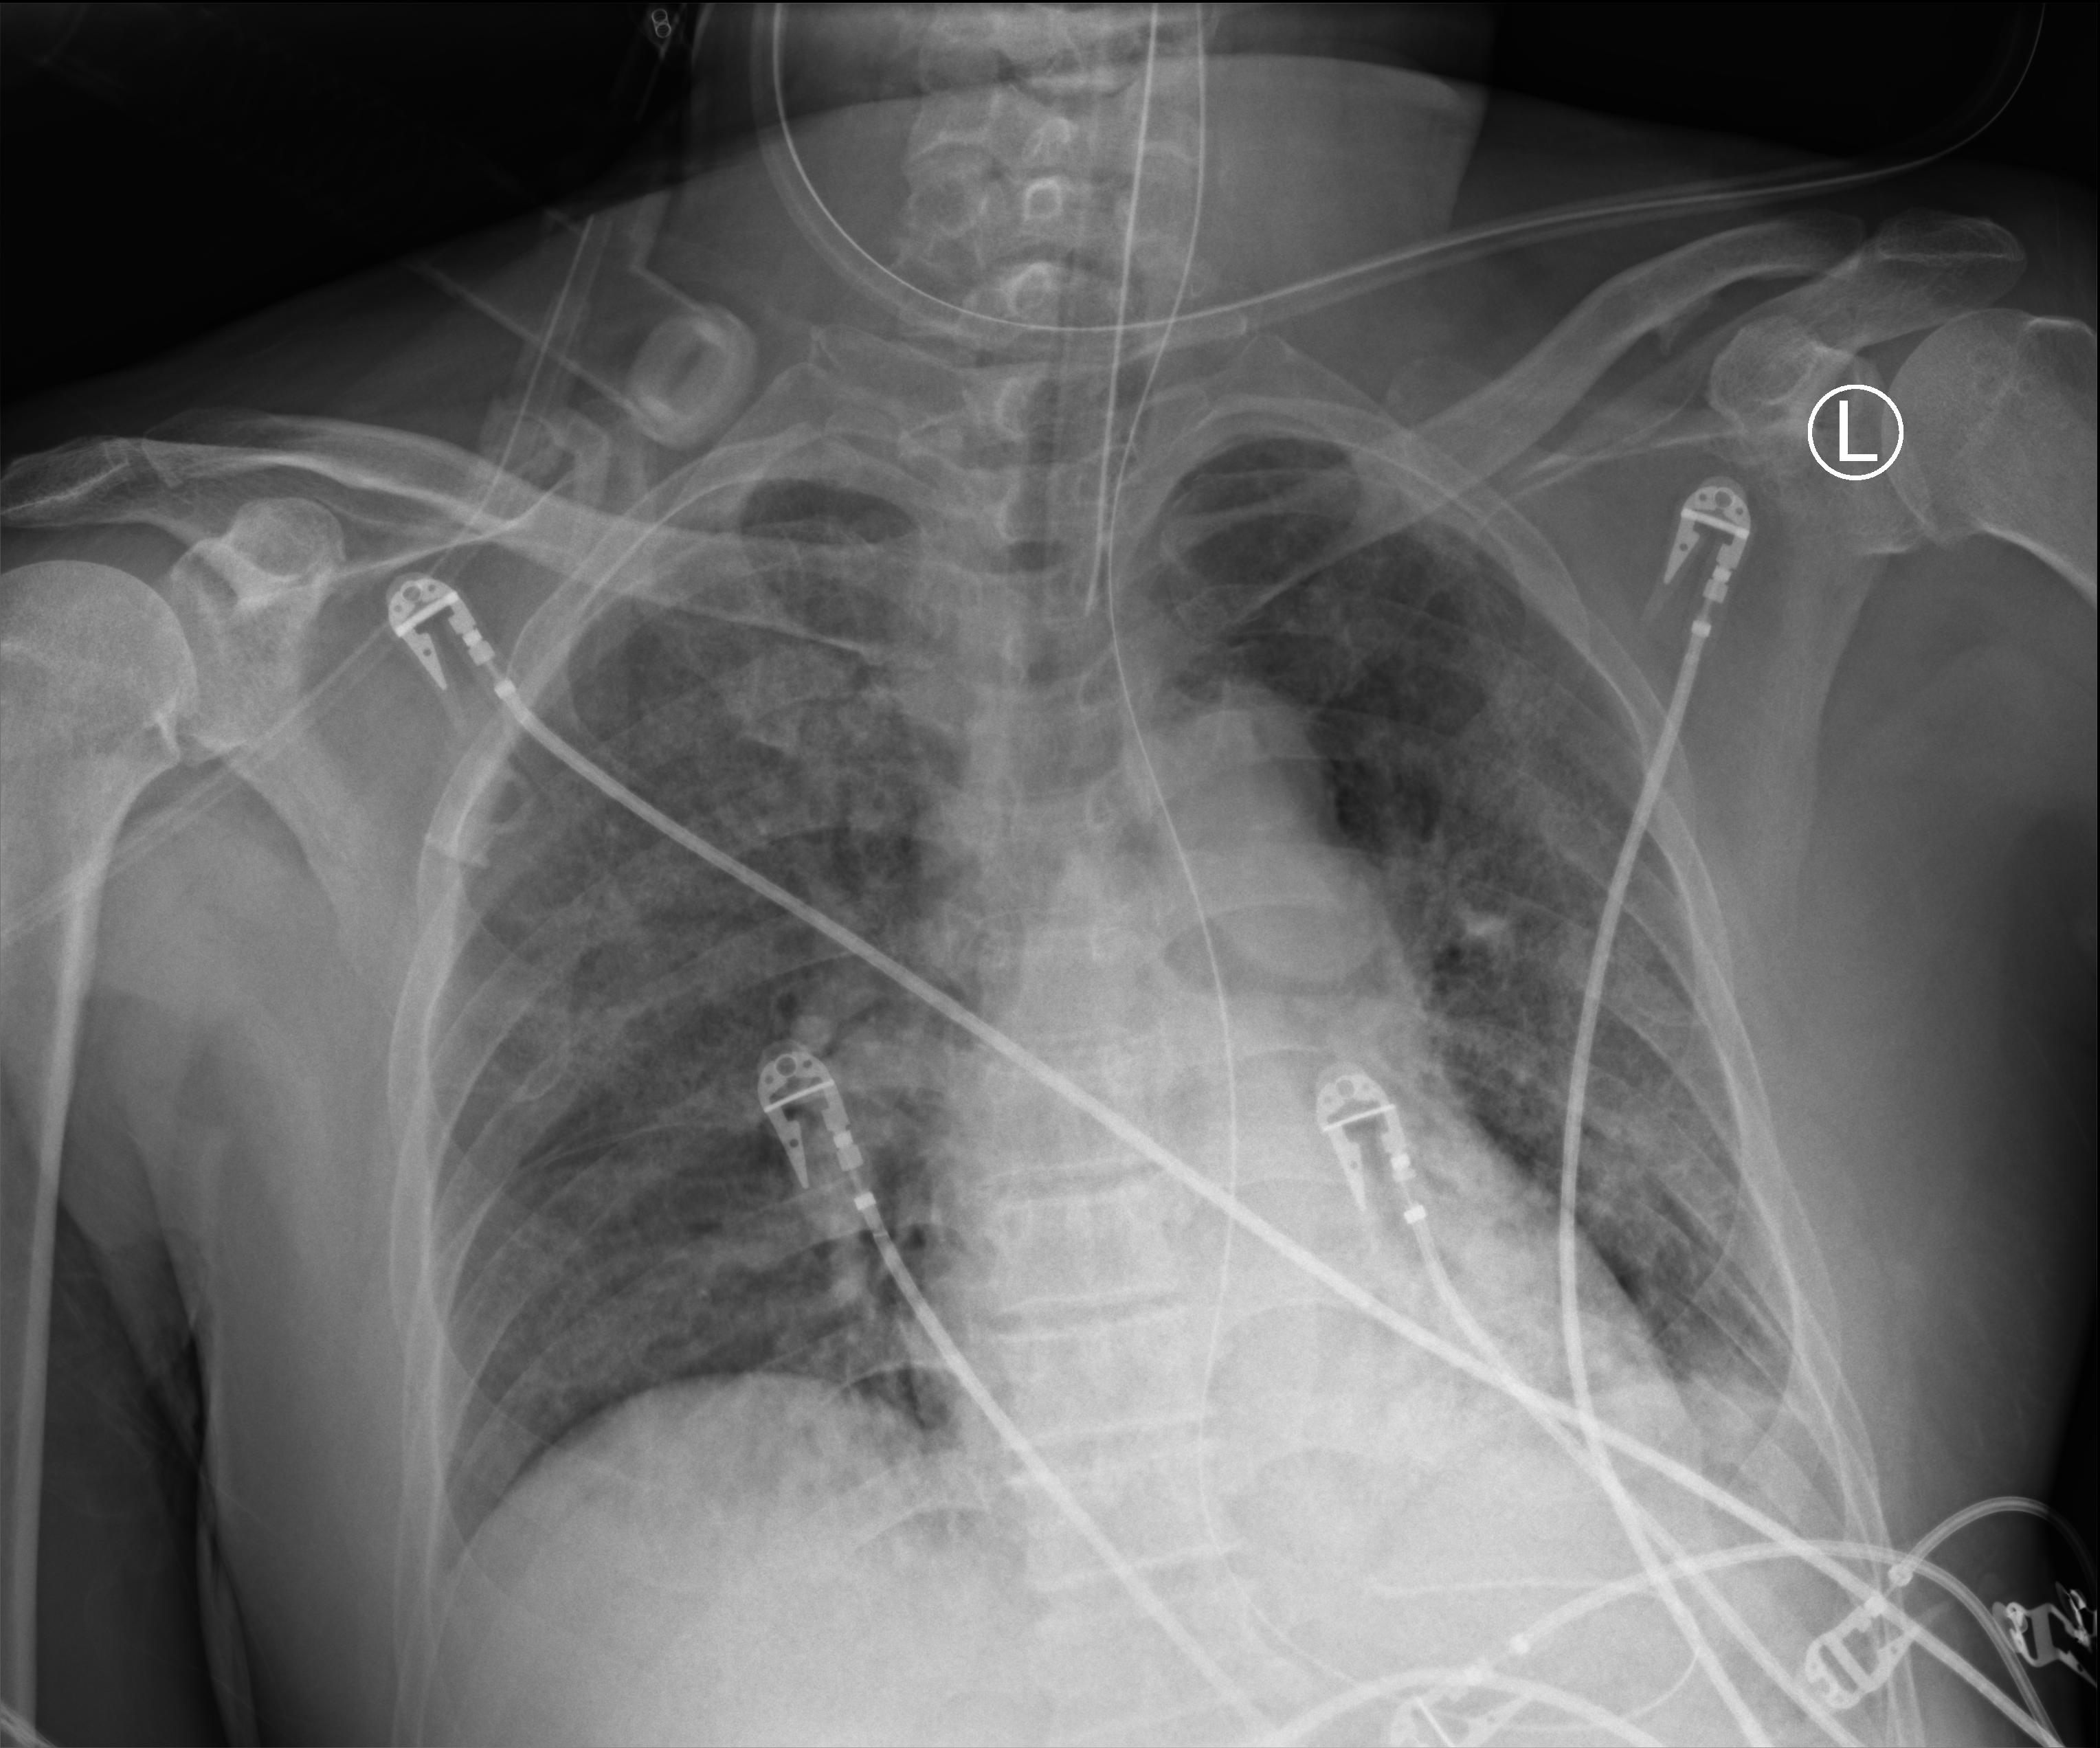
Portable chest radiograph, anteroposterior (AP) projection. Male patient hospitalised with COVID-19, age 60–74 years.
Admission-level facts for this patient (not findings on this image; timing relative to this image not recorded): admitted to intensive care during this hospital stay: yes; mechanically ventilated during this hospital stay: yes.